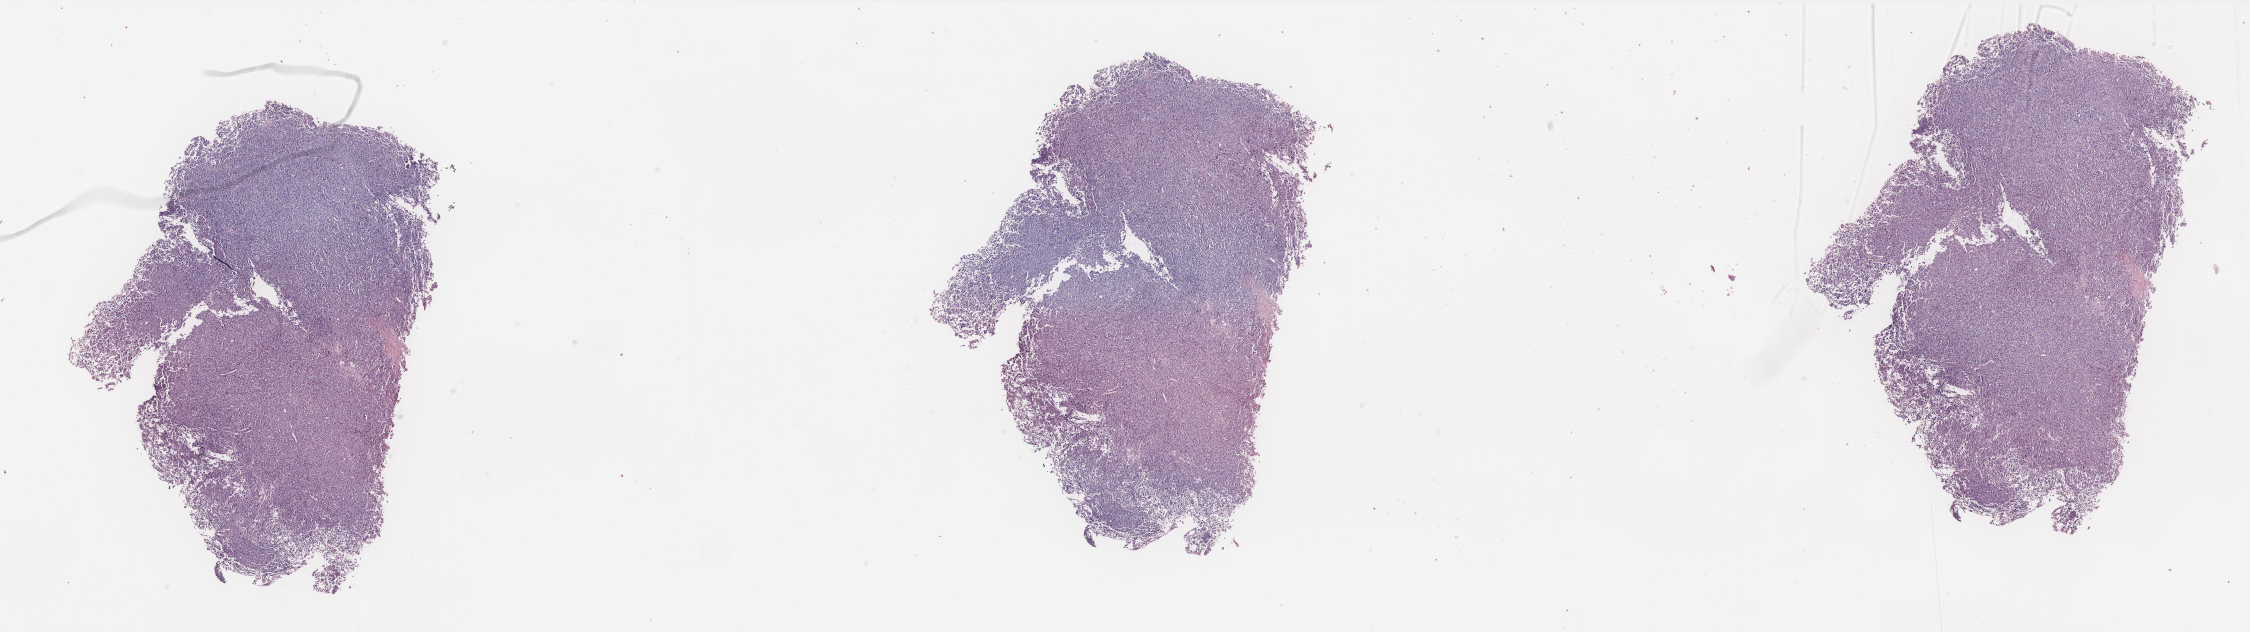
Whole-slide histology image, H&E-stained — a low-resolution overview of the entire scanned area, about 36.1 x 10.1 mm. FFPE section. Skin, primary tumour sample. Male, age 45 years at initial diagnosis.
Pathologic diagnosis: Malignant melanoma, NOS.